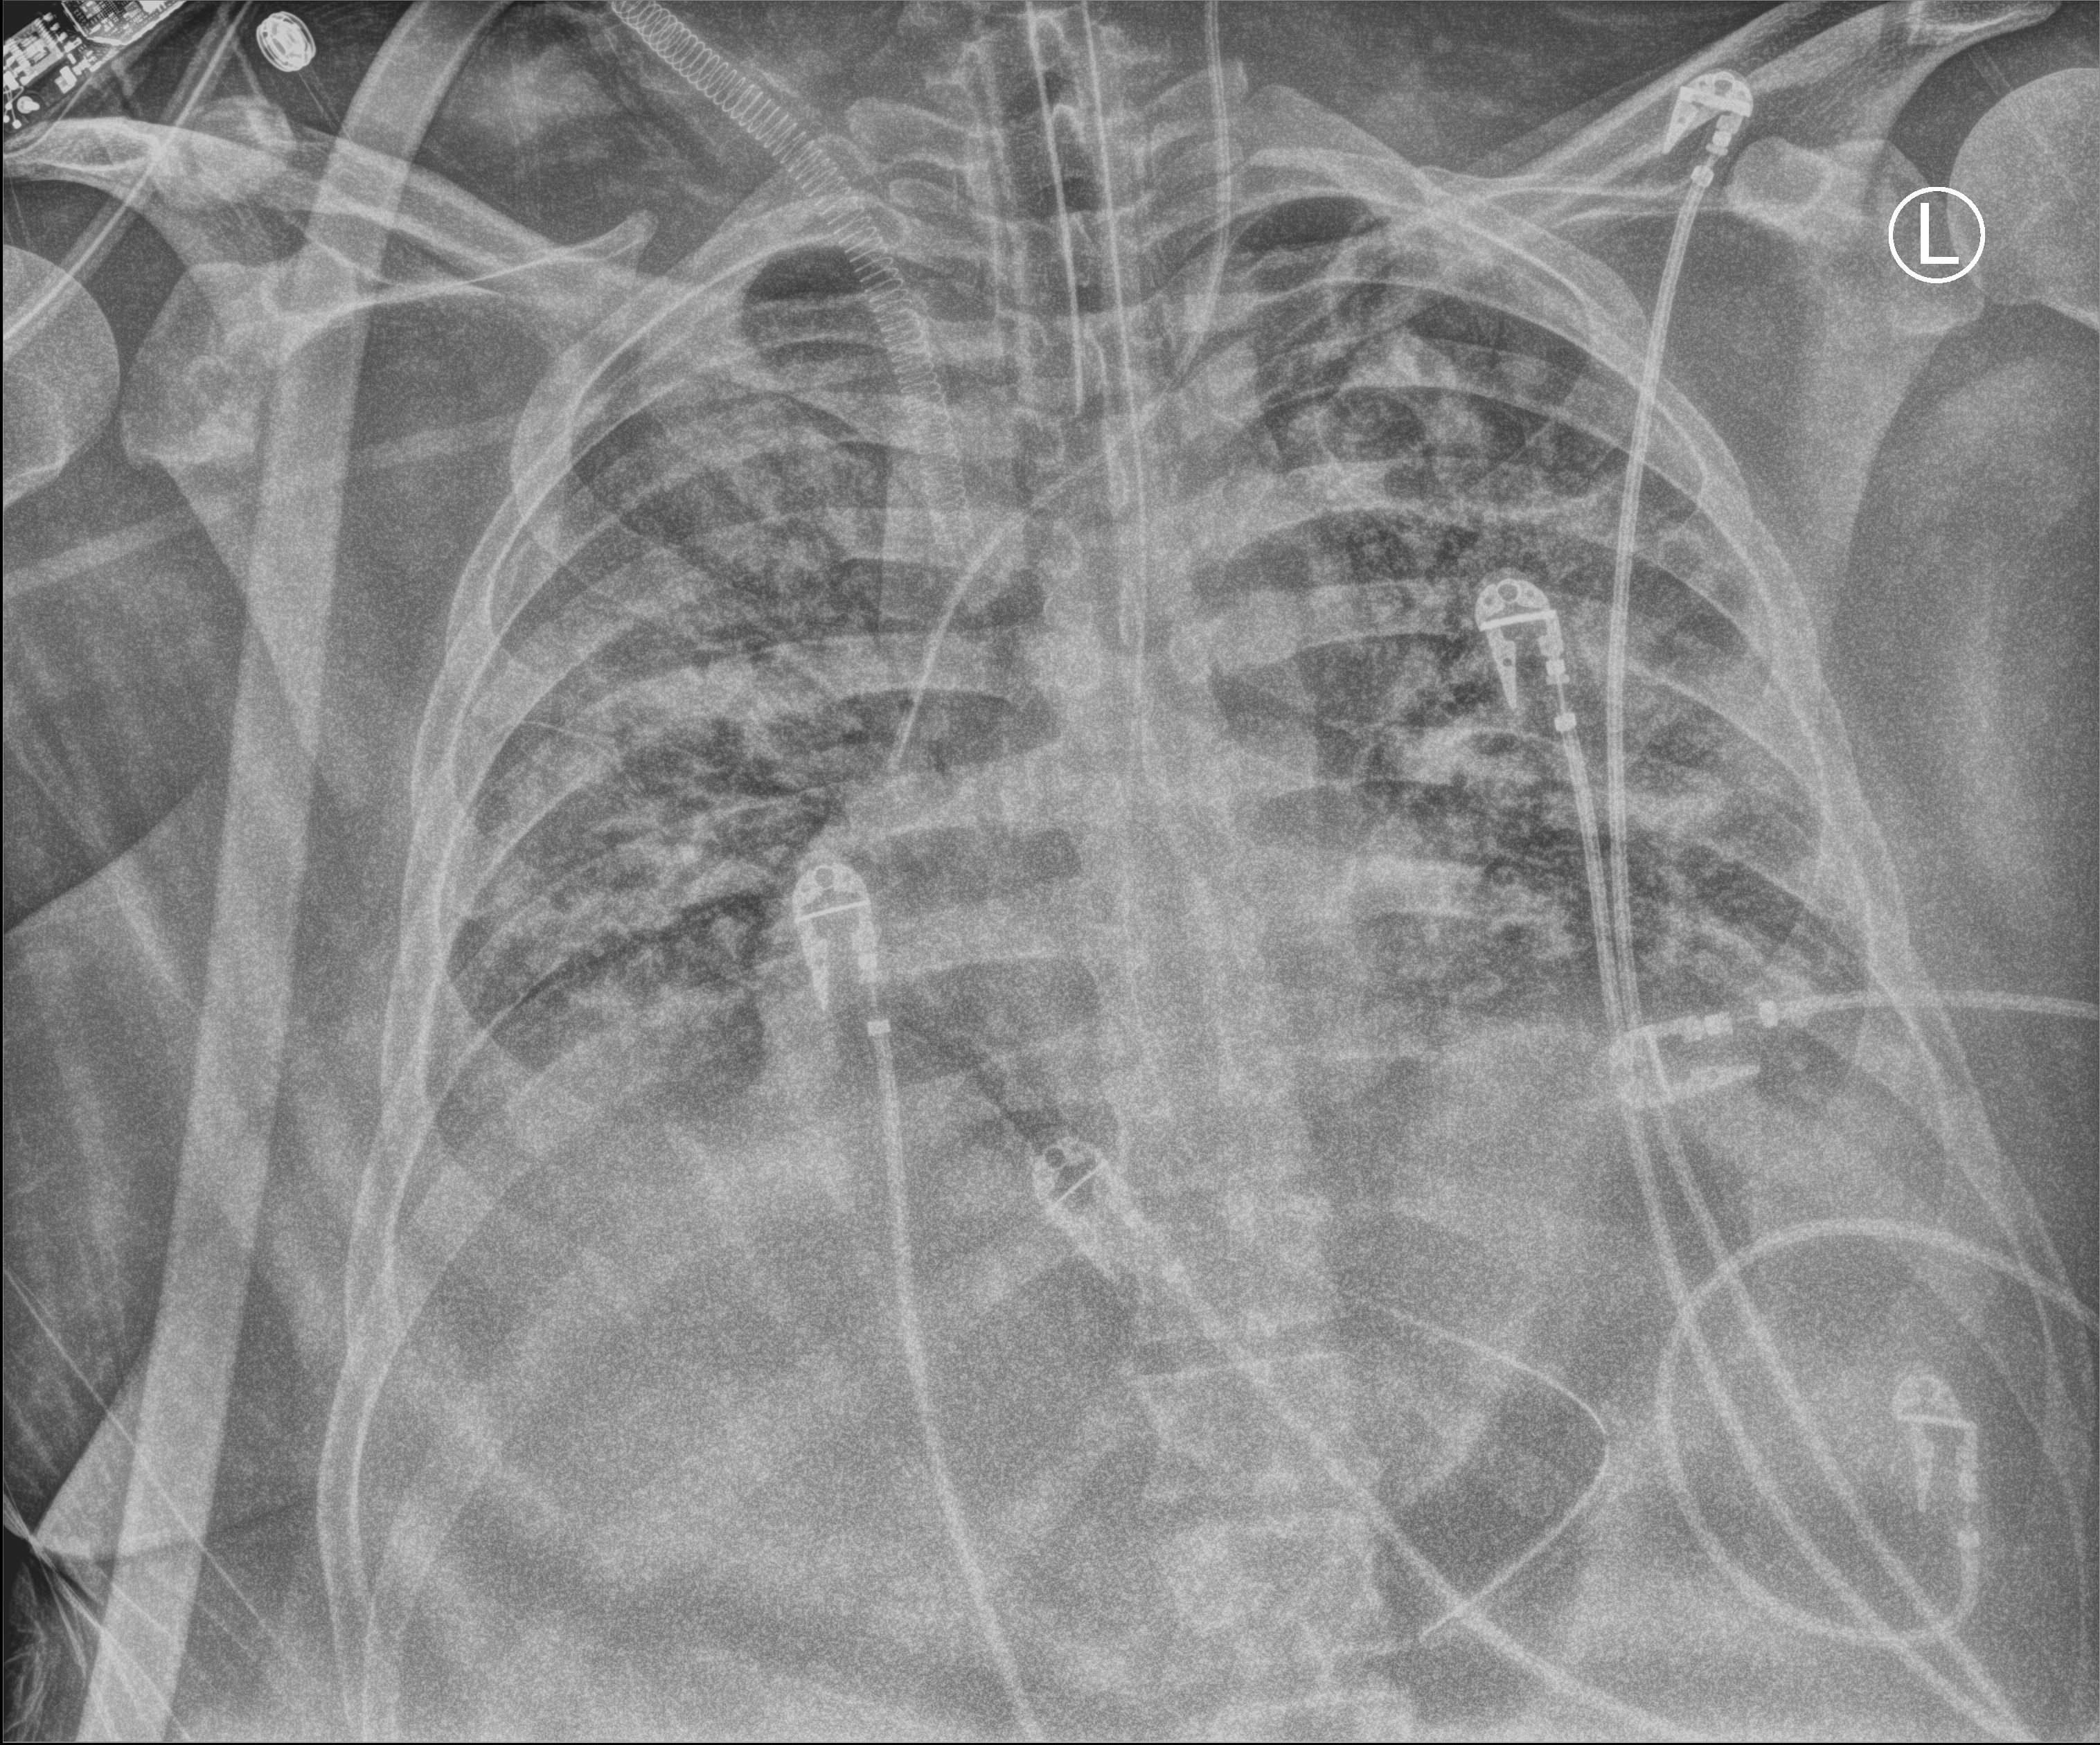
Portable chest radiograph, anteroposterior (AP) projection. Patient hospitalised with COVID-19, aged 18–59 years.
From the hospital-stay record, not from the radiograph (when in the stay this image was taken is not recorded): smoking status (admission record): never; length of hospital stay: 15 days; mechanically ventilated during this hospital stay: yes.